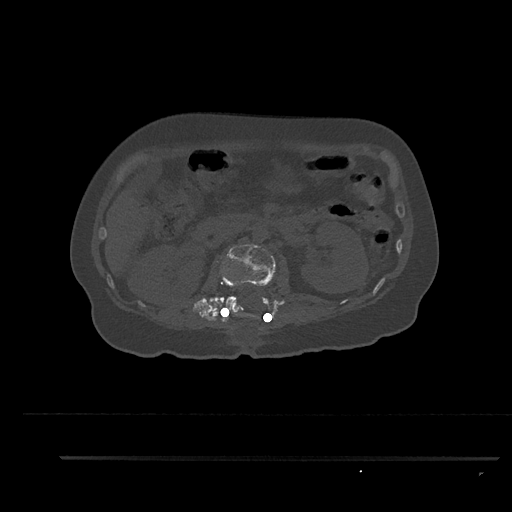
CT including the spine, one axial slice; reconstruction kernel Br40s/3; 120 kVp; bone window (W 1800 / L 400 HU); 0.5 mm slice thickness; 512 × 512 image matrix, field of view 408 × 408 mm. Patient: female, 44 years. From the clinical record (not read from this slice): primary cancer: renal; vertebrae with lytic lesions (as recorded): L1.
Annotated regions visible in this slice (semi-automatic segmentation, software-assisted and operator-edited):
- L1 vertebra: box from (x=221, y=266) to (x=242, y=317) px
- L2 vertebra: (x=224, y=244)–(x=274, y=316)